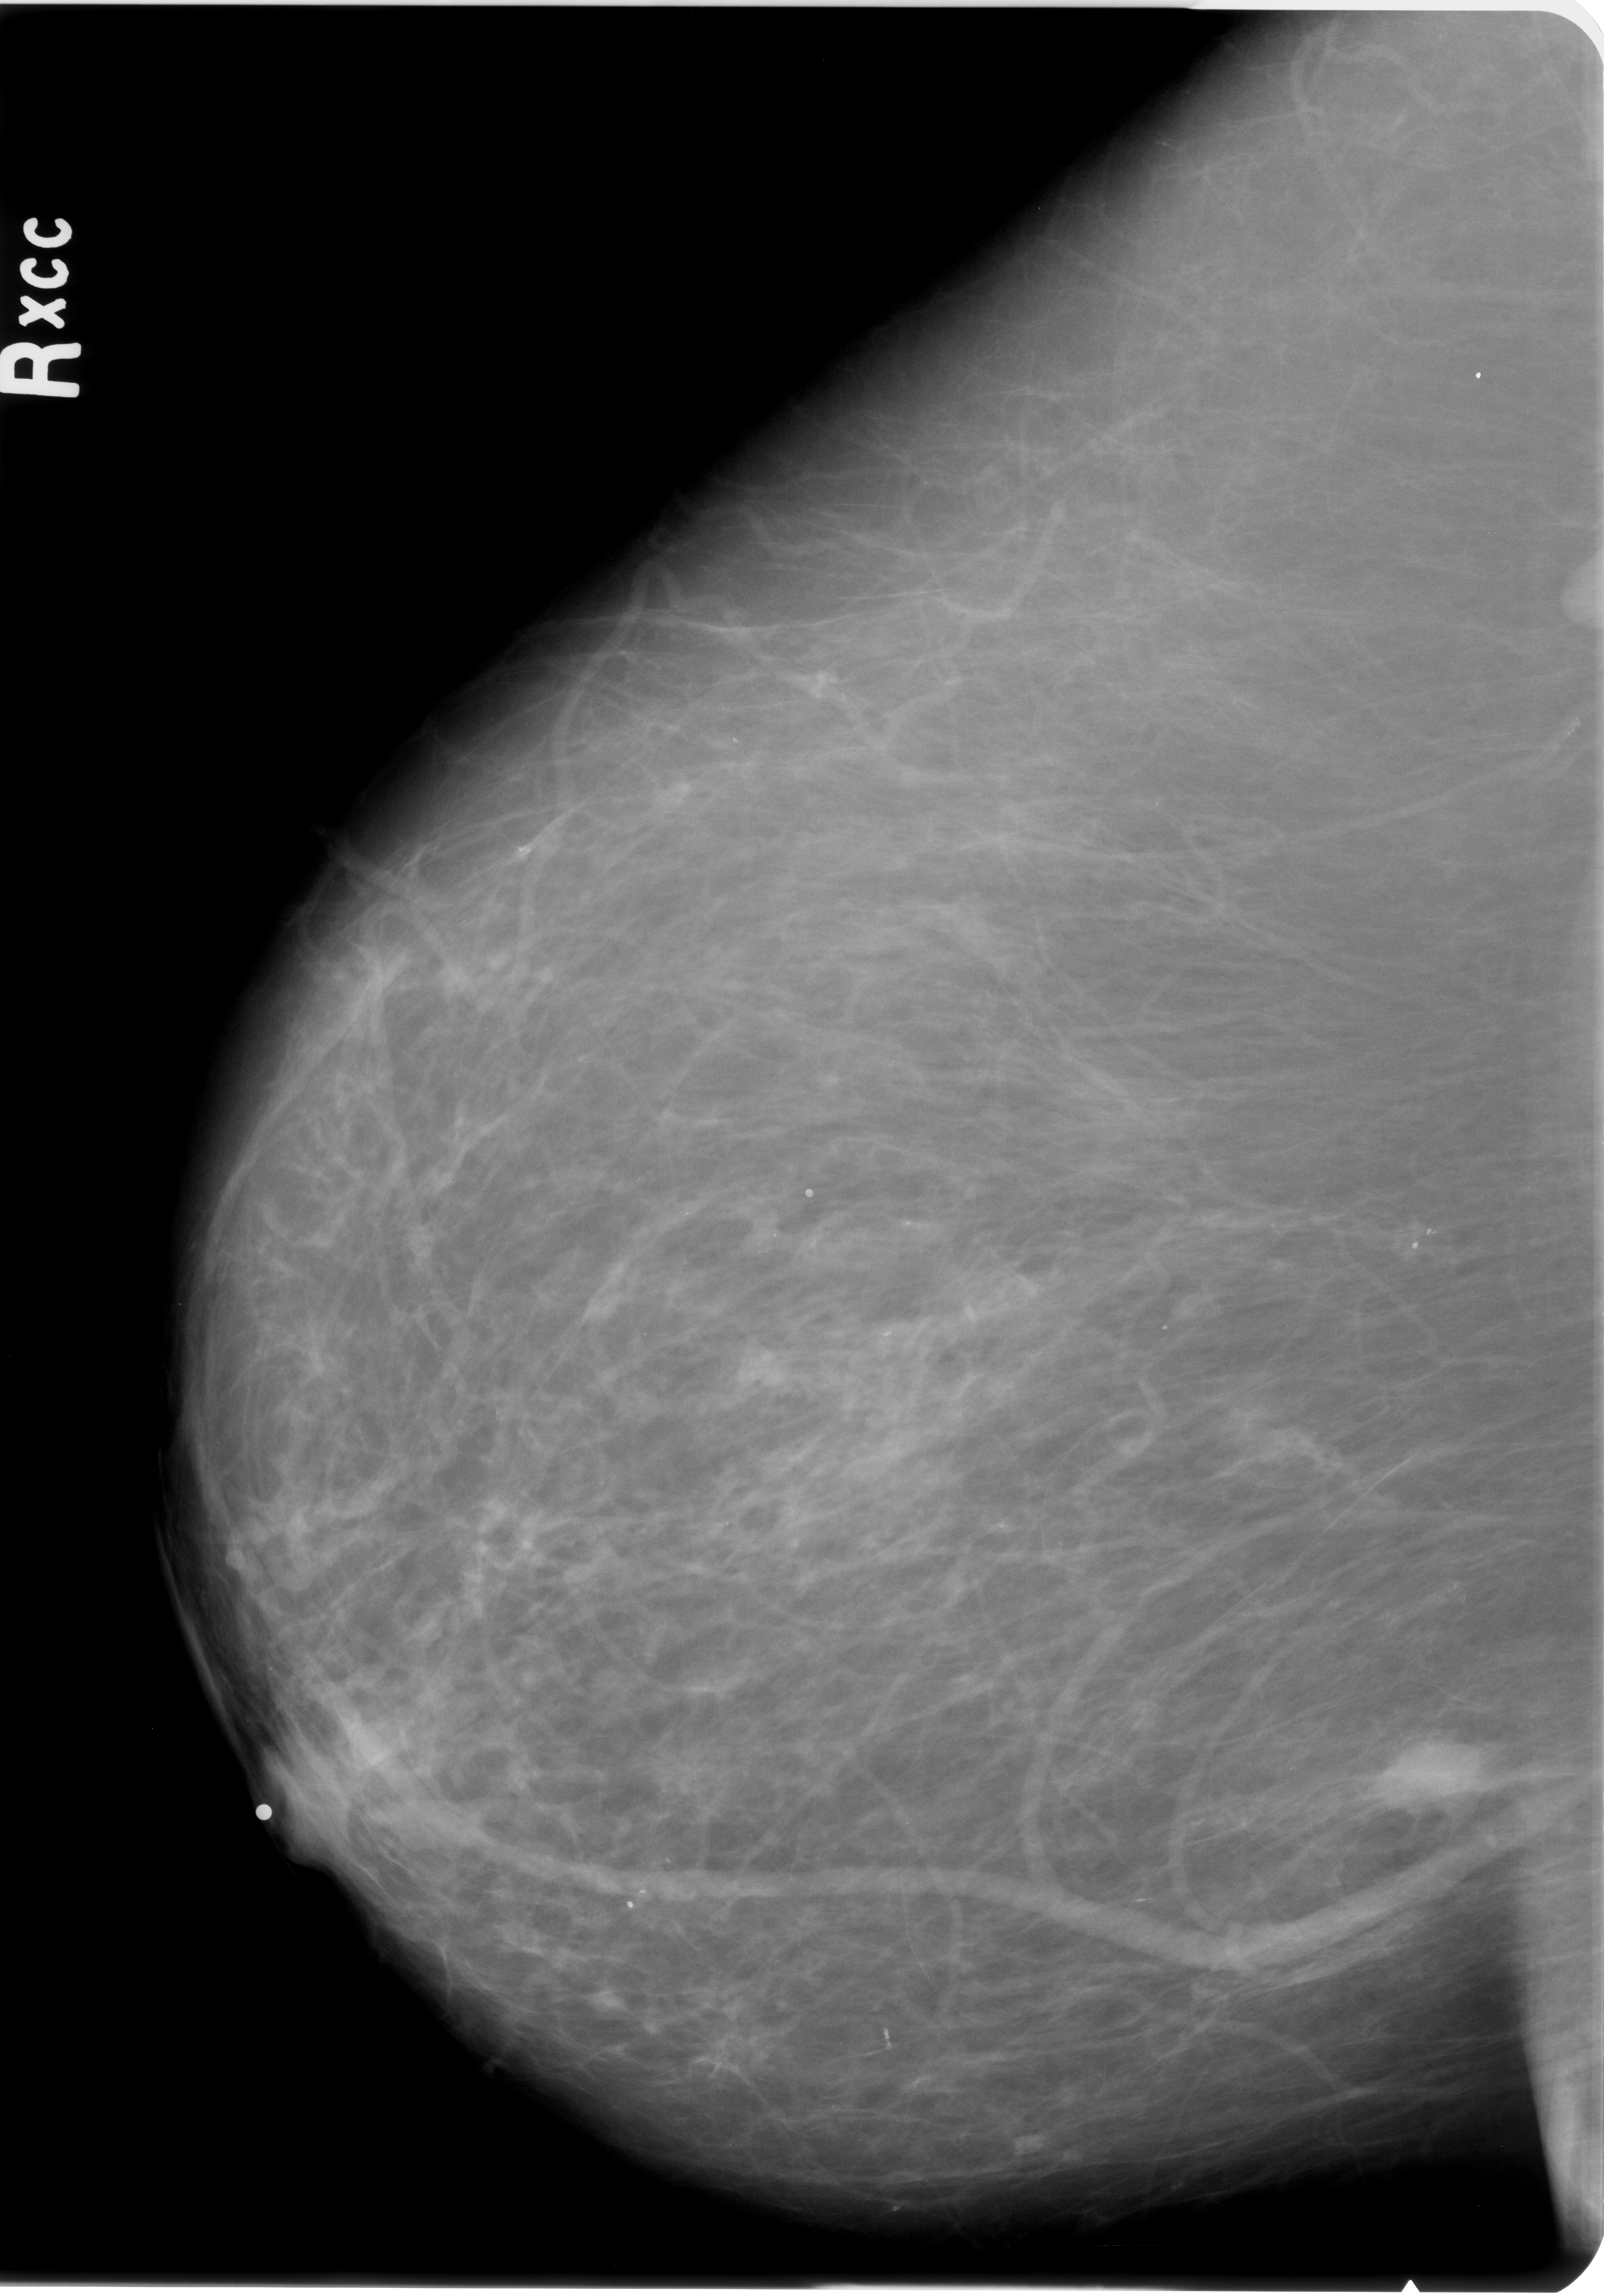
Digitized screen-film mammogram; right breast; craniocaudal (CC) view; BI-RADS breast density category 2 (scale 1–4).
Mass, shape irregular, margins spiculated; BI-RADS assessment category 4; subtlety rating 5 on a 1 (subtle) to 5 (obvious) scale; pathology (as recorded): malignant.